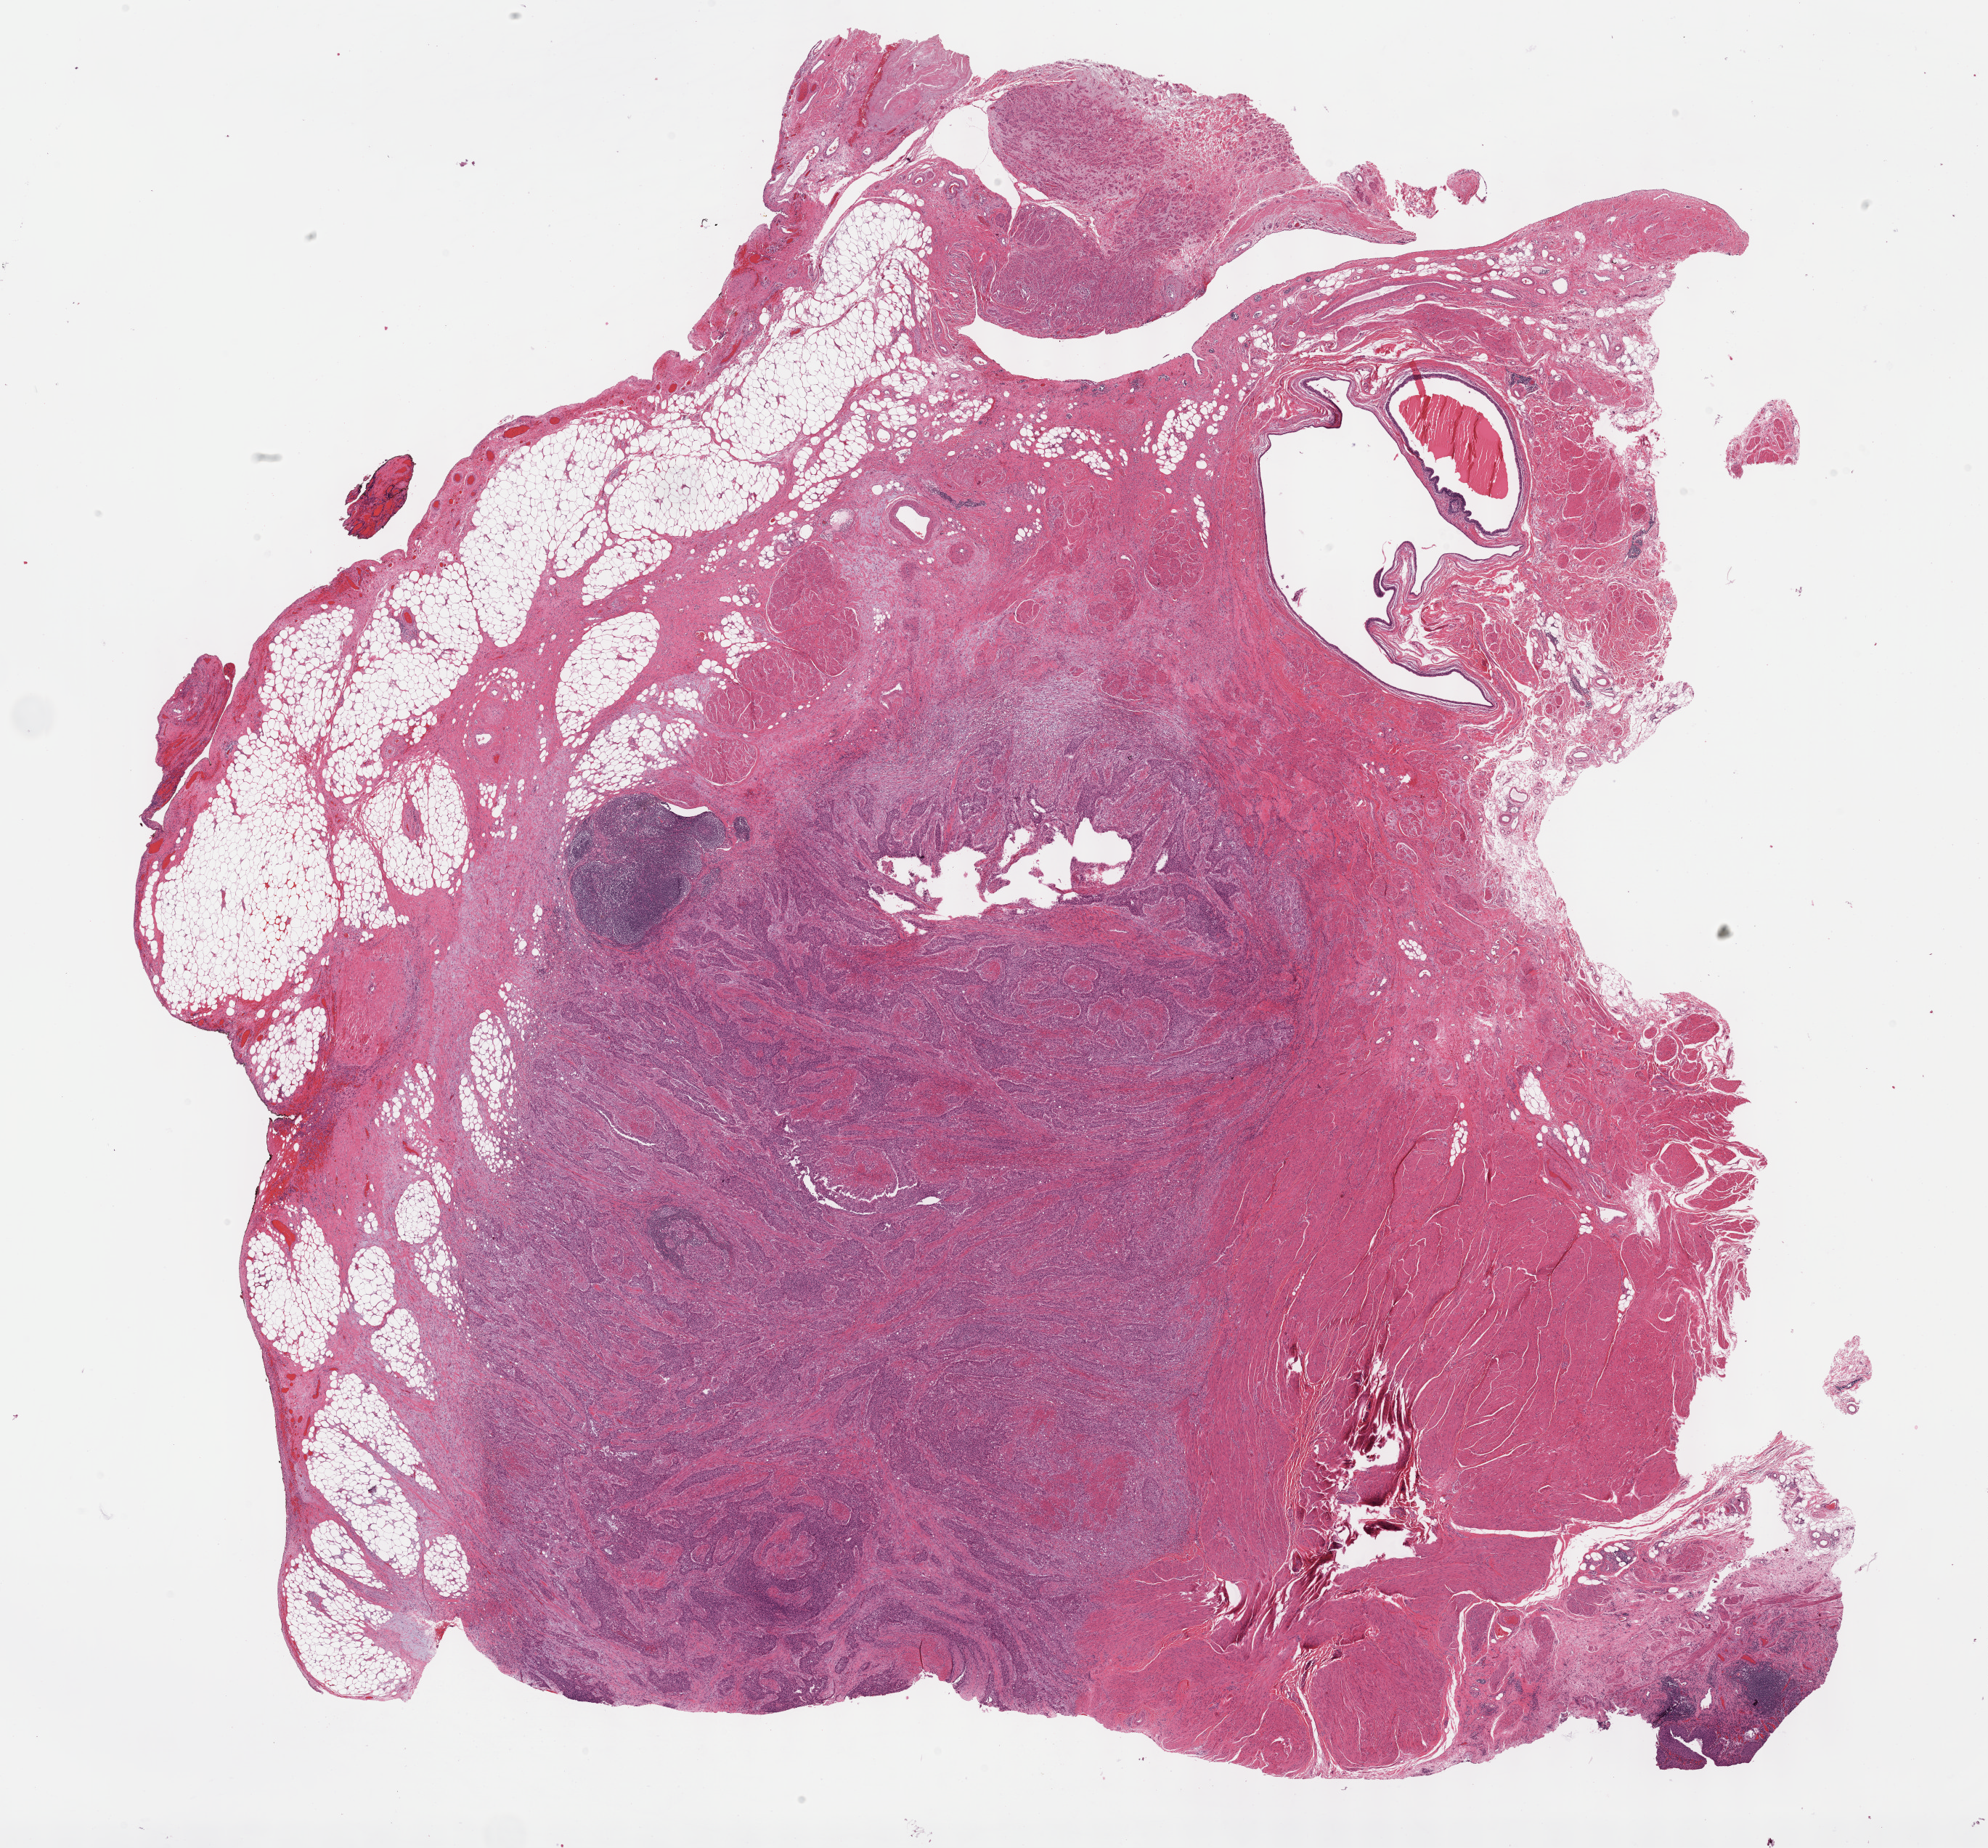
Digitized H&E-stained tissue section (whole slide) — a low-resolution overview of the entire scanned area, about 22.1 x 20.6 mm (slide scanned at 40x). Formalin-fixed paraffin-embedded (FFPE) diagnostic section. Sample: primary tumour, bladder. Female patient; age at initial diagnosis 63 years.
Histologic diagnosis: Transitional cell carcinoma (posterior wall of bladder).